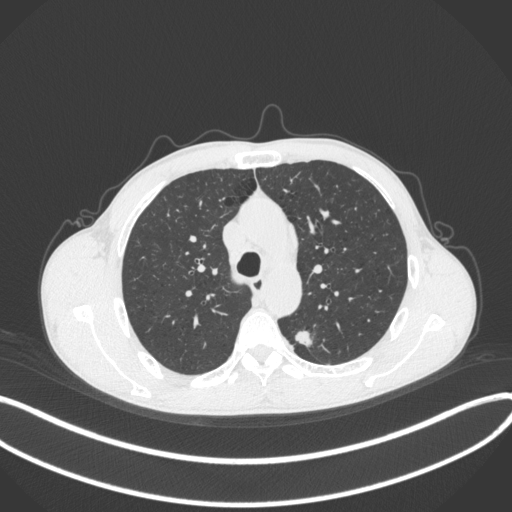
Chest CT, one axial slice. Slice 281 of 429 in the series (ordered by position). Reconstruction kernel B31f. Lung window (W 1500 / L -600 HU). 512 × 512 image matrix, field of view 400 × 400 mm. Patient: male, 51 years. From the clinical record (not read from this slice): clinical TNM (as recorded): T2a N1 M1.
Annotated regions visible in this slice (rectangle marked by the reading radiologist):
- lung tumour (recorded histology: adenocarcinoma): bounding box (x1, y1, x2, y2) in pixels: (292, 324, 319, 348)